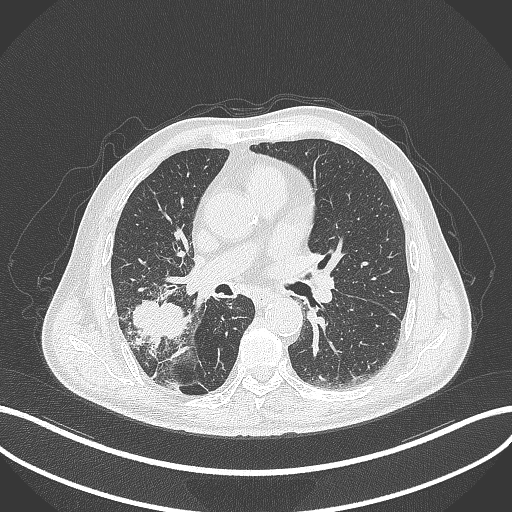
Chest CT, one axial slice. Slice 226 of 429 in the series (ordered by position). Reconstruction kernel B70f. Lung window (W 1500 / L -600 HU). 1 mm slice thickness. 512 × 512 image matrix, field of view 400 × 400 mm. Male patient, age 72 years. From the clinical record (not read from this slice): clinical TNM (as recorded): T3 N2 M0.
Annotated regions visible in this slice (bounding box drawn by a radiologist):
- lung tumour (recorded histology: adenocarcinoma): bounding box <128,298,186,348> (left, top, right, bottom; pixels)